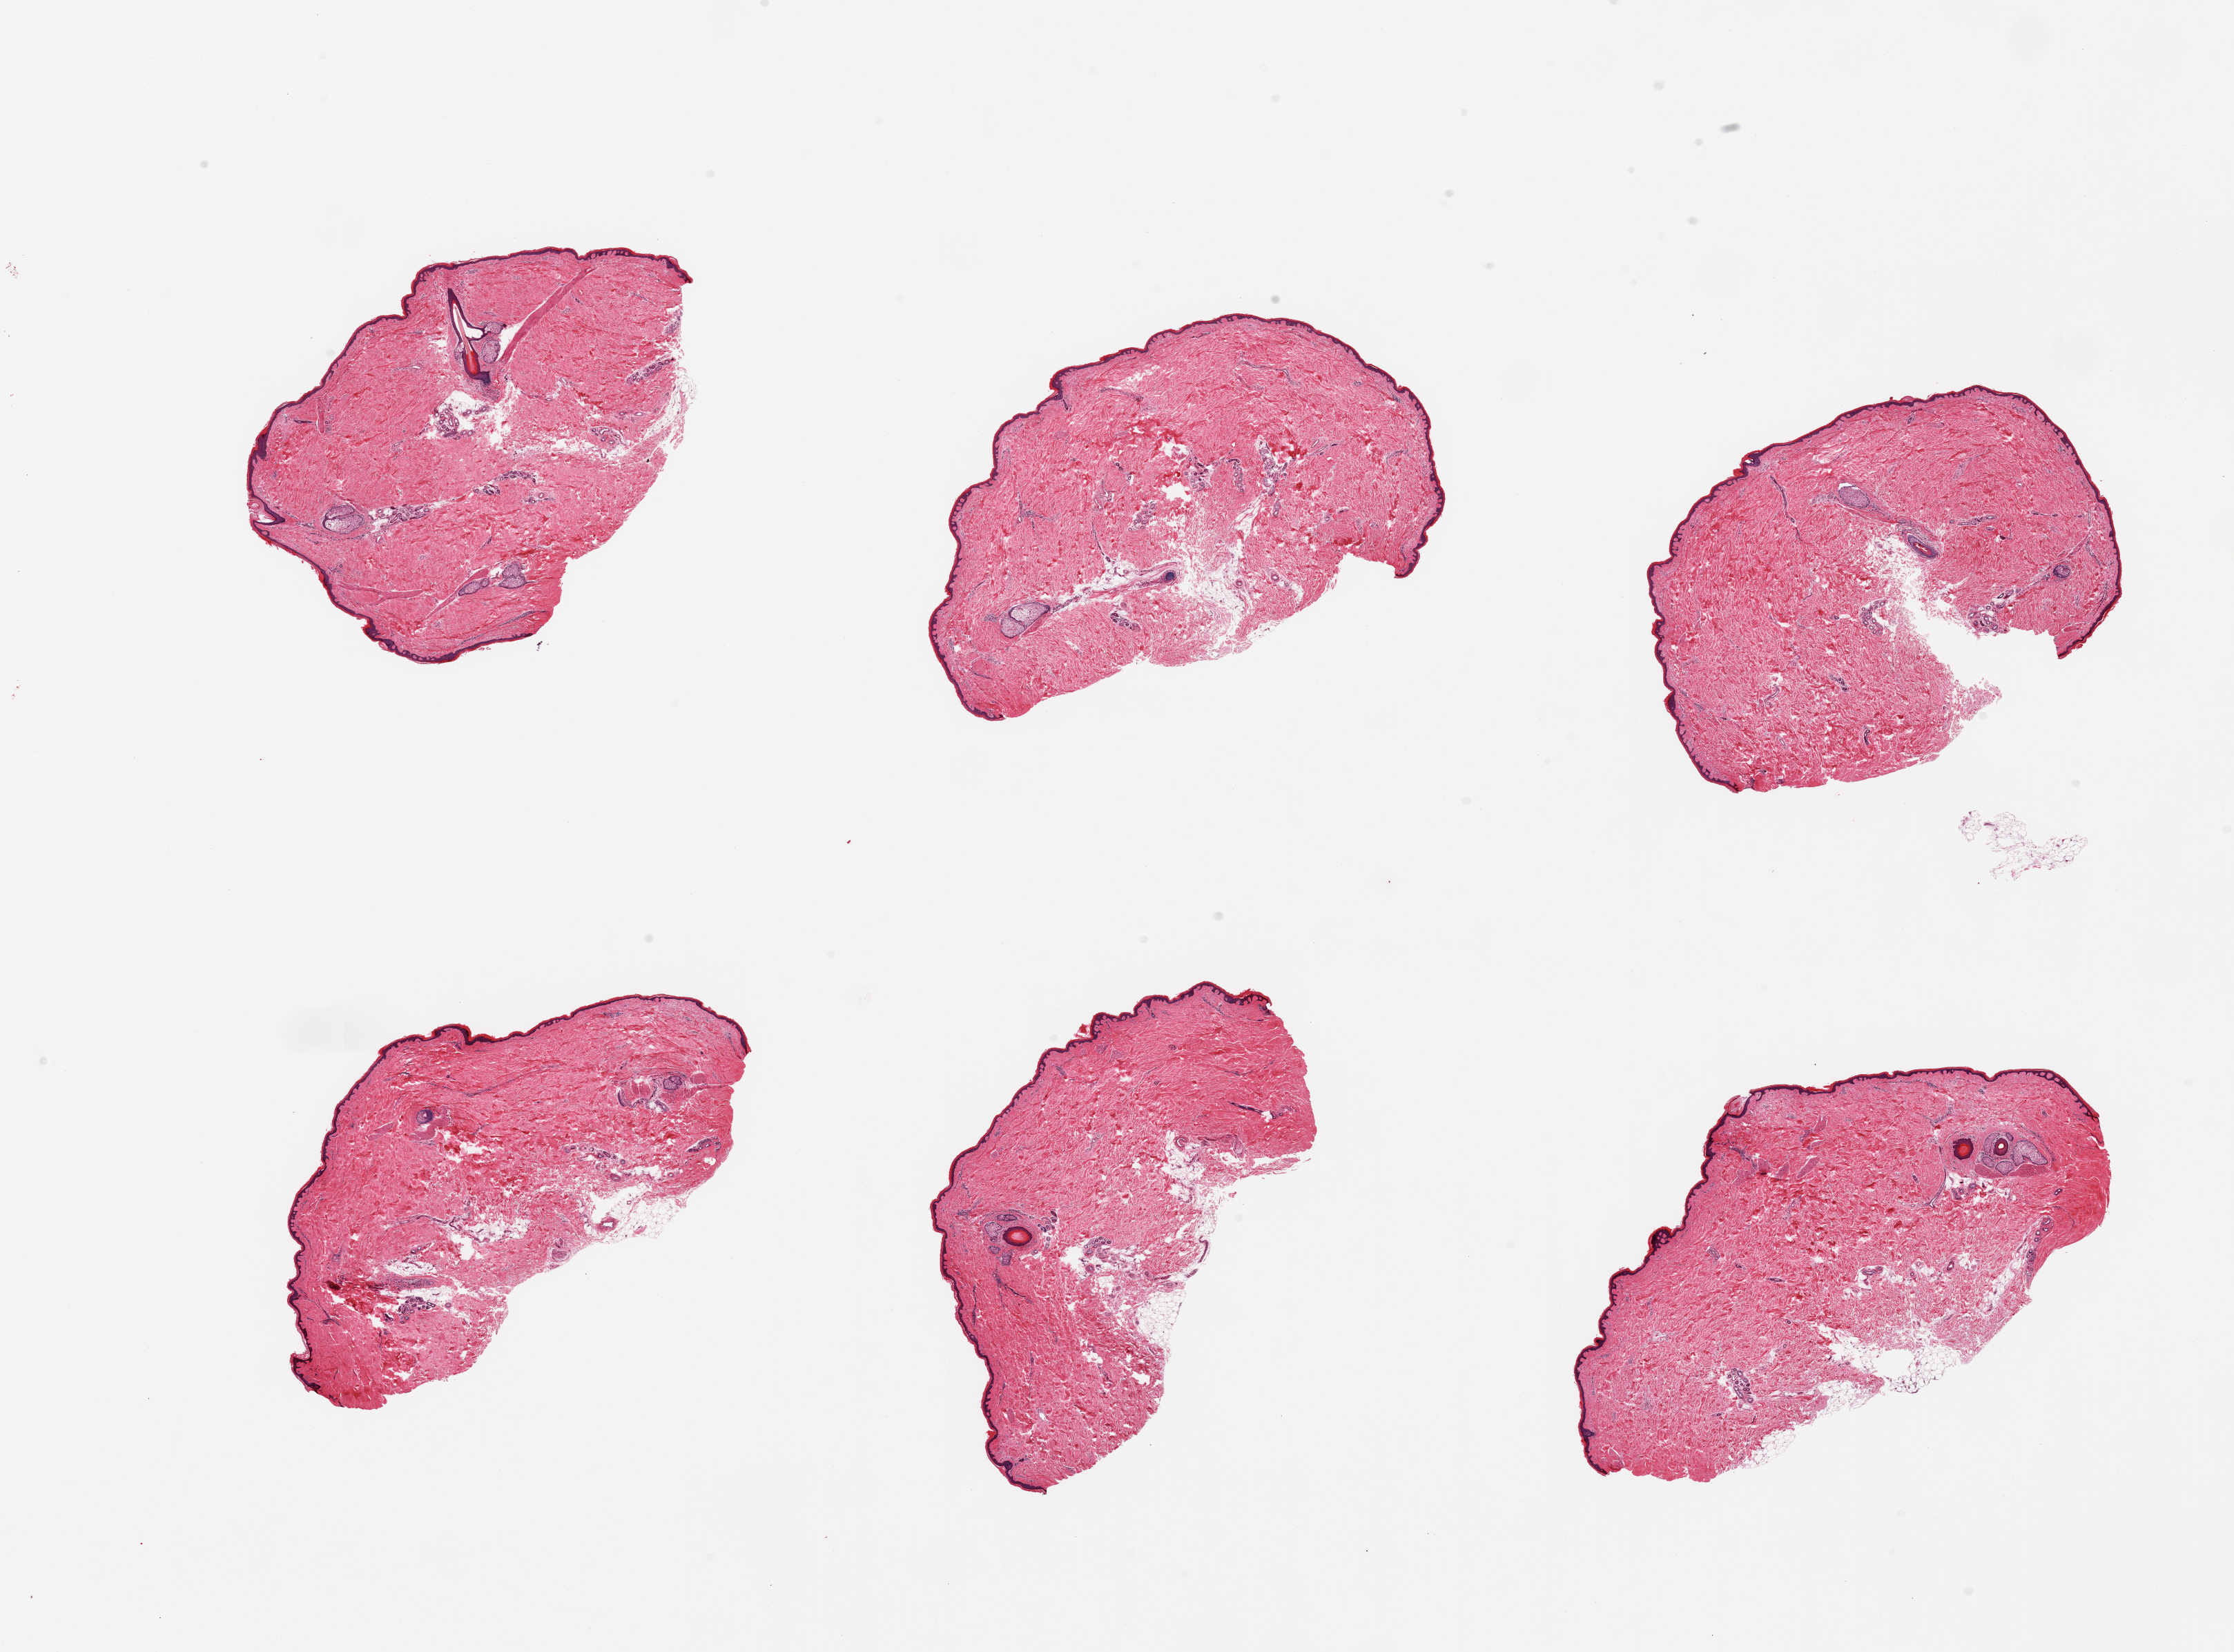
H&E whole-slide image, shown as a low-resolution overview of the whole scanned area (about 25.6 x 18.9 mm, acquisition: 20x scan); PAXgene-fixed paraffin-embedded (PFPE) section; sampled site (target tissue): skin of lower leg; tissue donor sample.
Review note (as recorded): 6 pieces; relatively well trimmed, epidermis measures up to 35 microns.